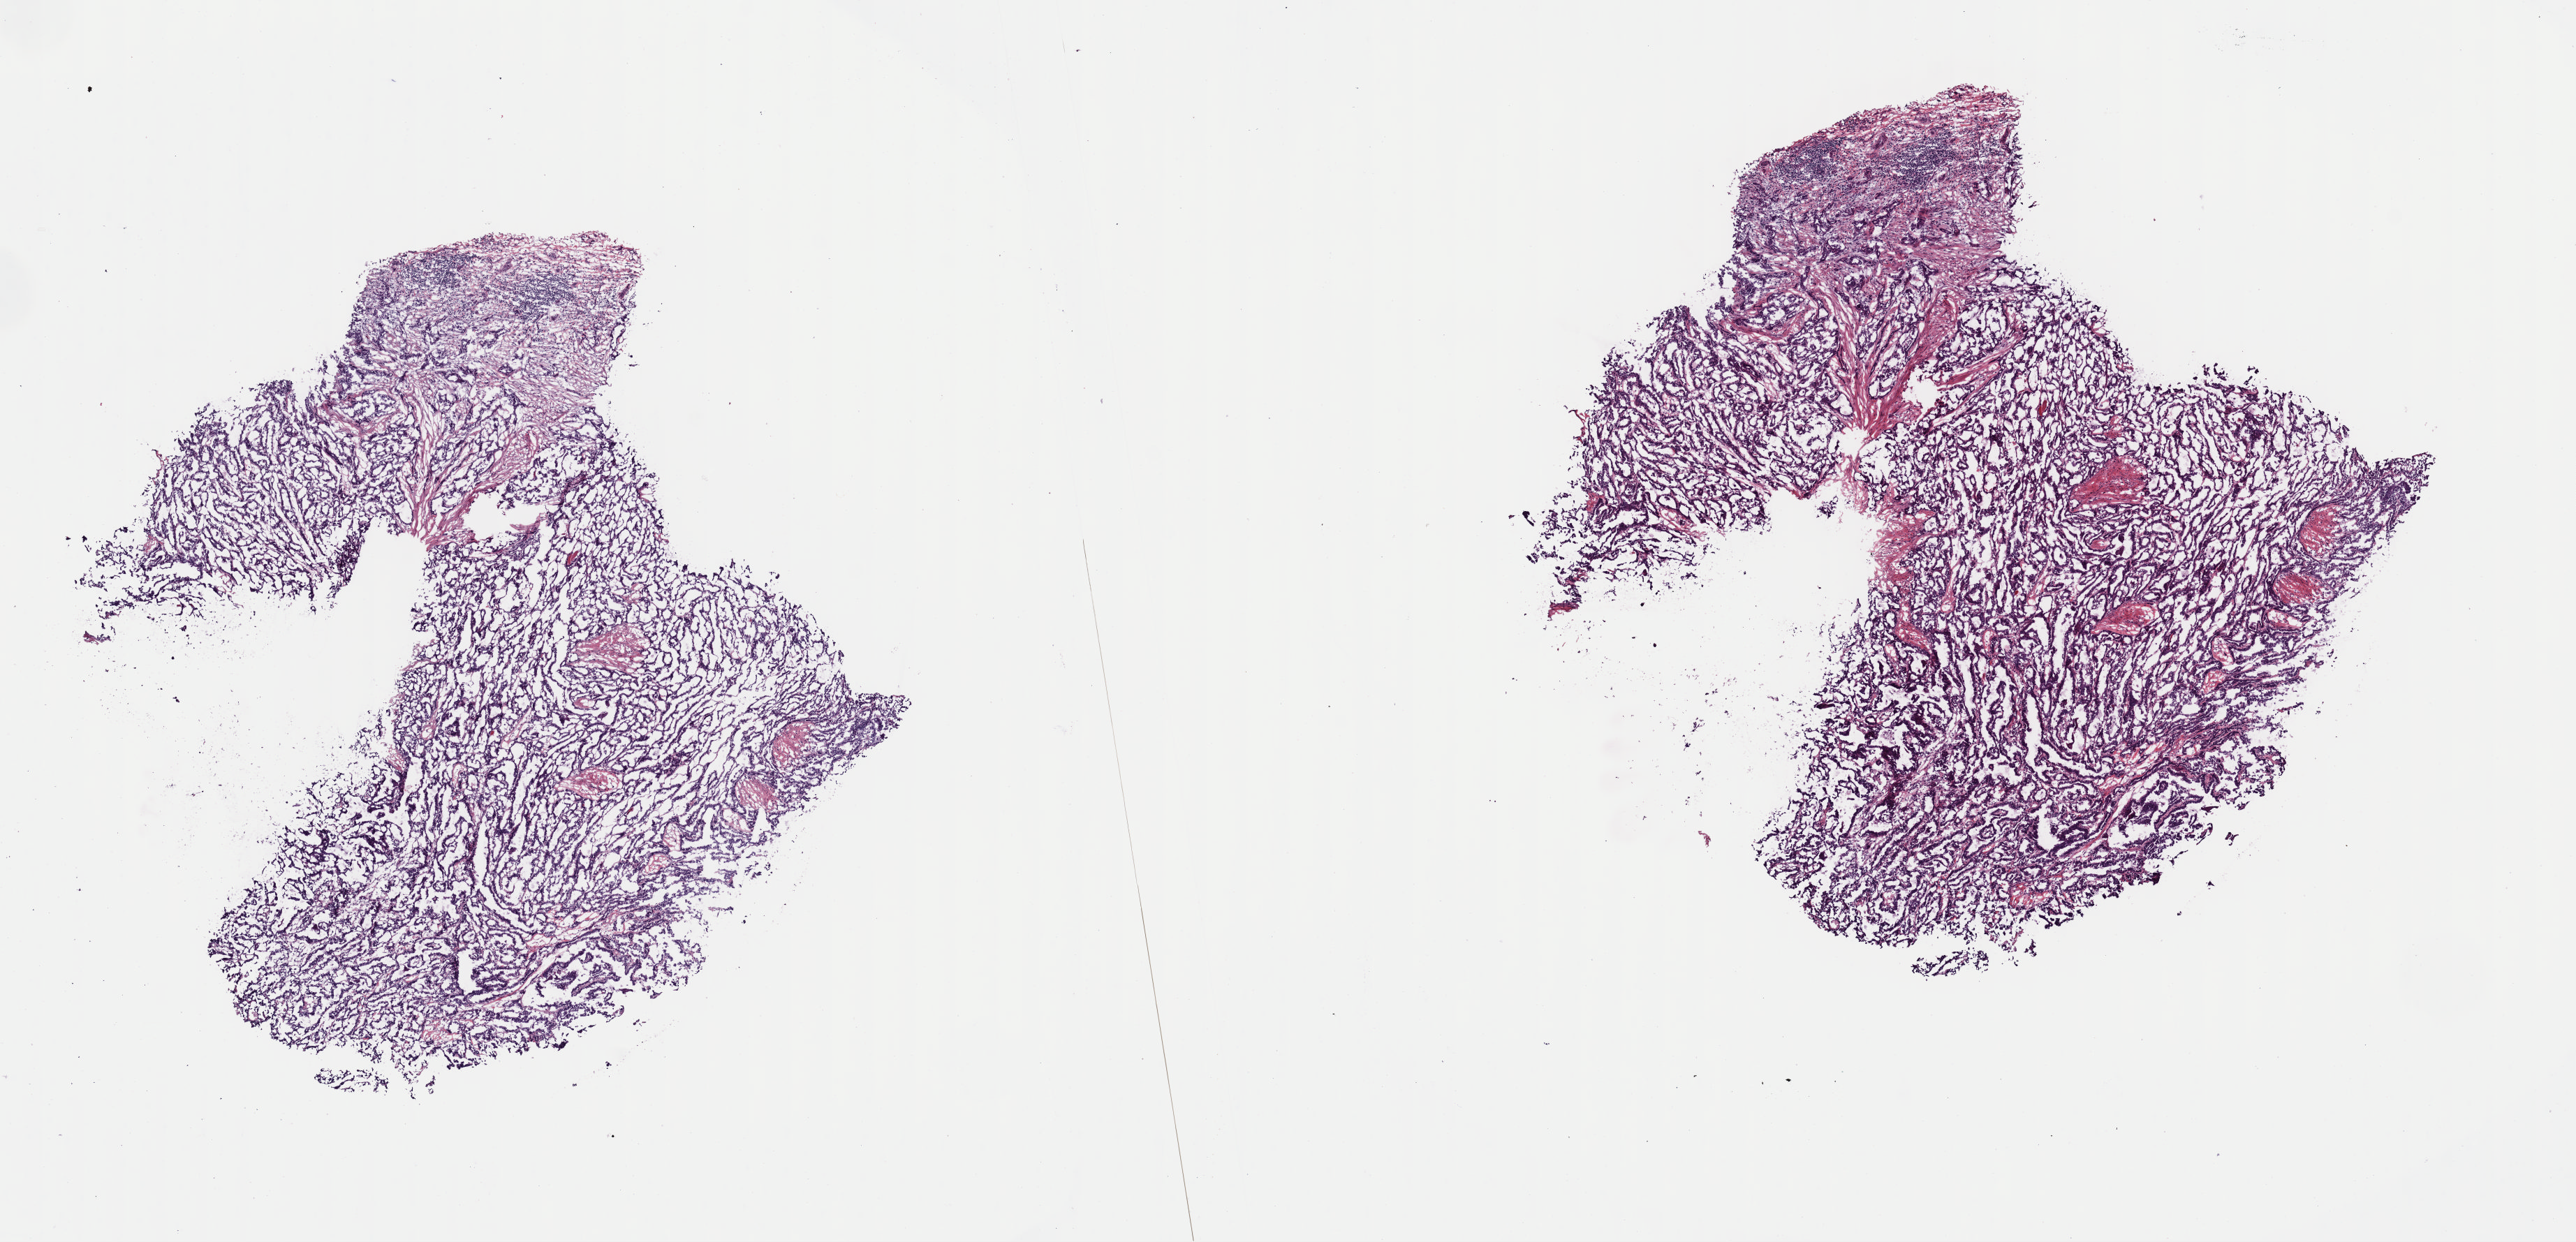
Digitized H&E-stained tissue section (whole slide) — low-resolution overview of the scanned area, about 14.6 x 7.0 mm. Frozen section. Thyroid, primary tumour sample. Female, age 55 years at initial diagnosis. Pathologist review of this section (percent, as recorded): tumour cells 90%, tumour nuclei 80%, normal cells 0%, stromal cells 10%, necrosis 0%. Infiltration values recorded for this section: lymphocyte infiltration 2%, monocyte infiltration 1%, neutrophil infiltration 0%.
Laterality: midline. Pathologic diagnosis: Papillary adenocarcinoma, NOS (thyroid gland). Lymph nodes positive (case pathology): 6 of 23 examined. AJCC pathologic stage: III (6th edition).